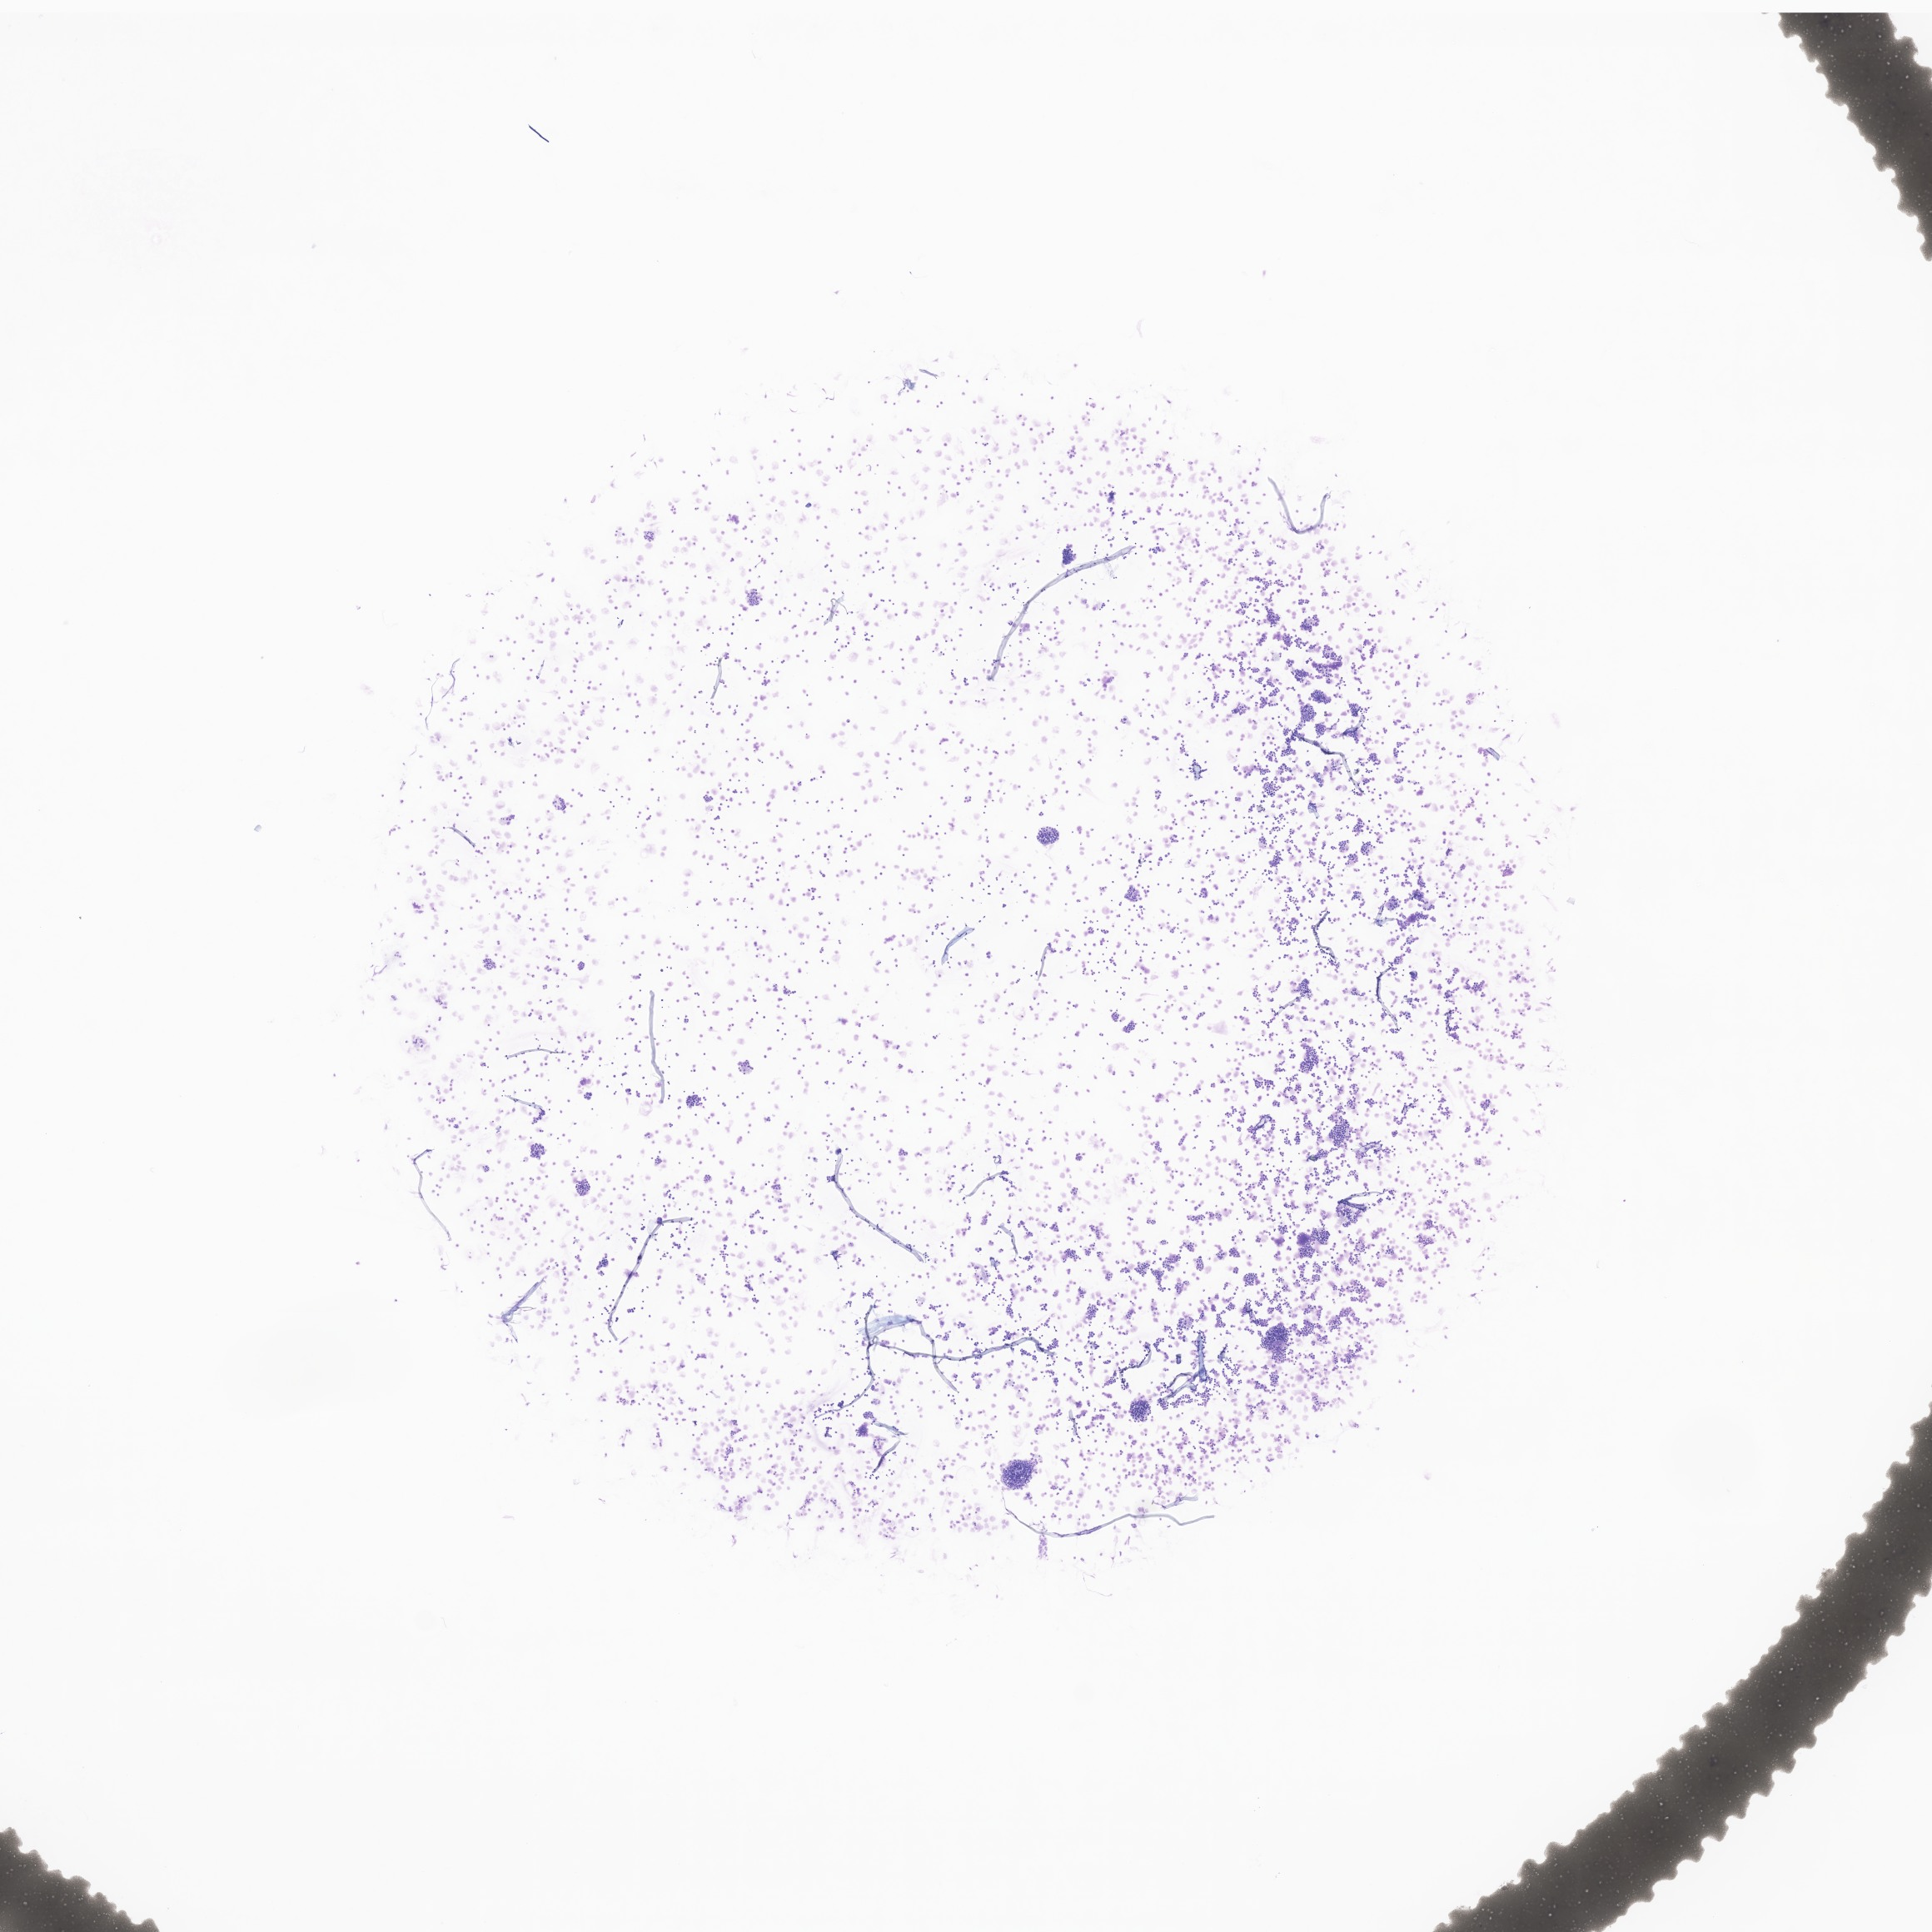
Whole-slide image of tumor tissue from the retroperitoneum — a low-resolution overview of the entire scanned area, about 9.8 x 9.8 mm. Male patient, age 41 months (3 years 5 months).
Recorded diagnosis: Neuroblastoma, NOS.